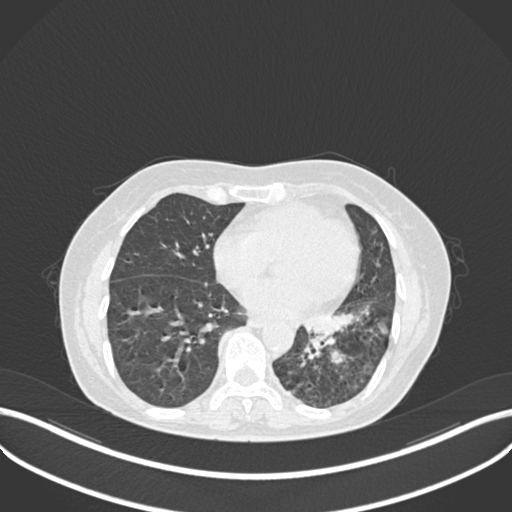
Chest CT, one axial slice. Position 102 of 270 along the scan axis. 120 kVp. Lung window (W 1500 / L -600 HU). 1 mm slice thickness. 512 × 512 image matrix, field of view 400 × 400 mm. Patient: female, 63 years. From the clinical record (not read from this slice): clinical TNM (as recorded): T1b N0 M0; histopathological grade: G2-3.
Outlined on this slice (rectangle marked by the reading radiologist):
- lung tumour (recorded histology: adenocarcinoma): bounding box <299,311,391,338> (left, top, right, bottom; pixels)